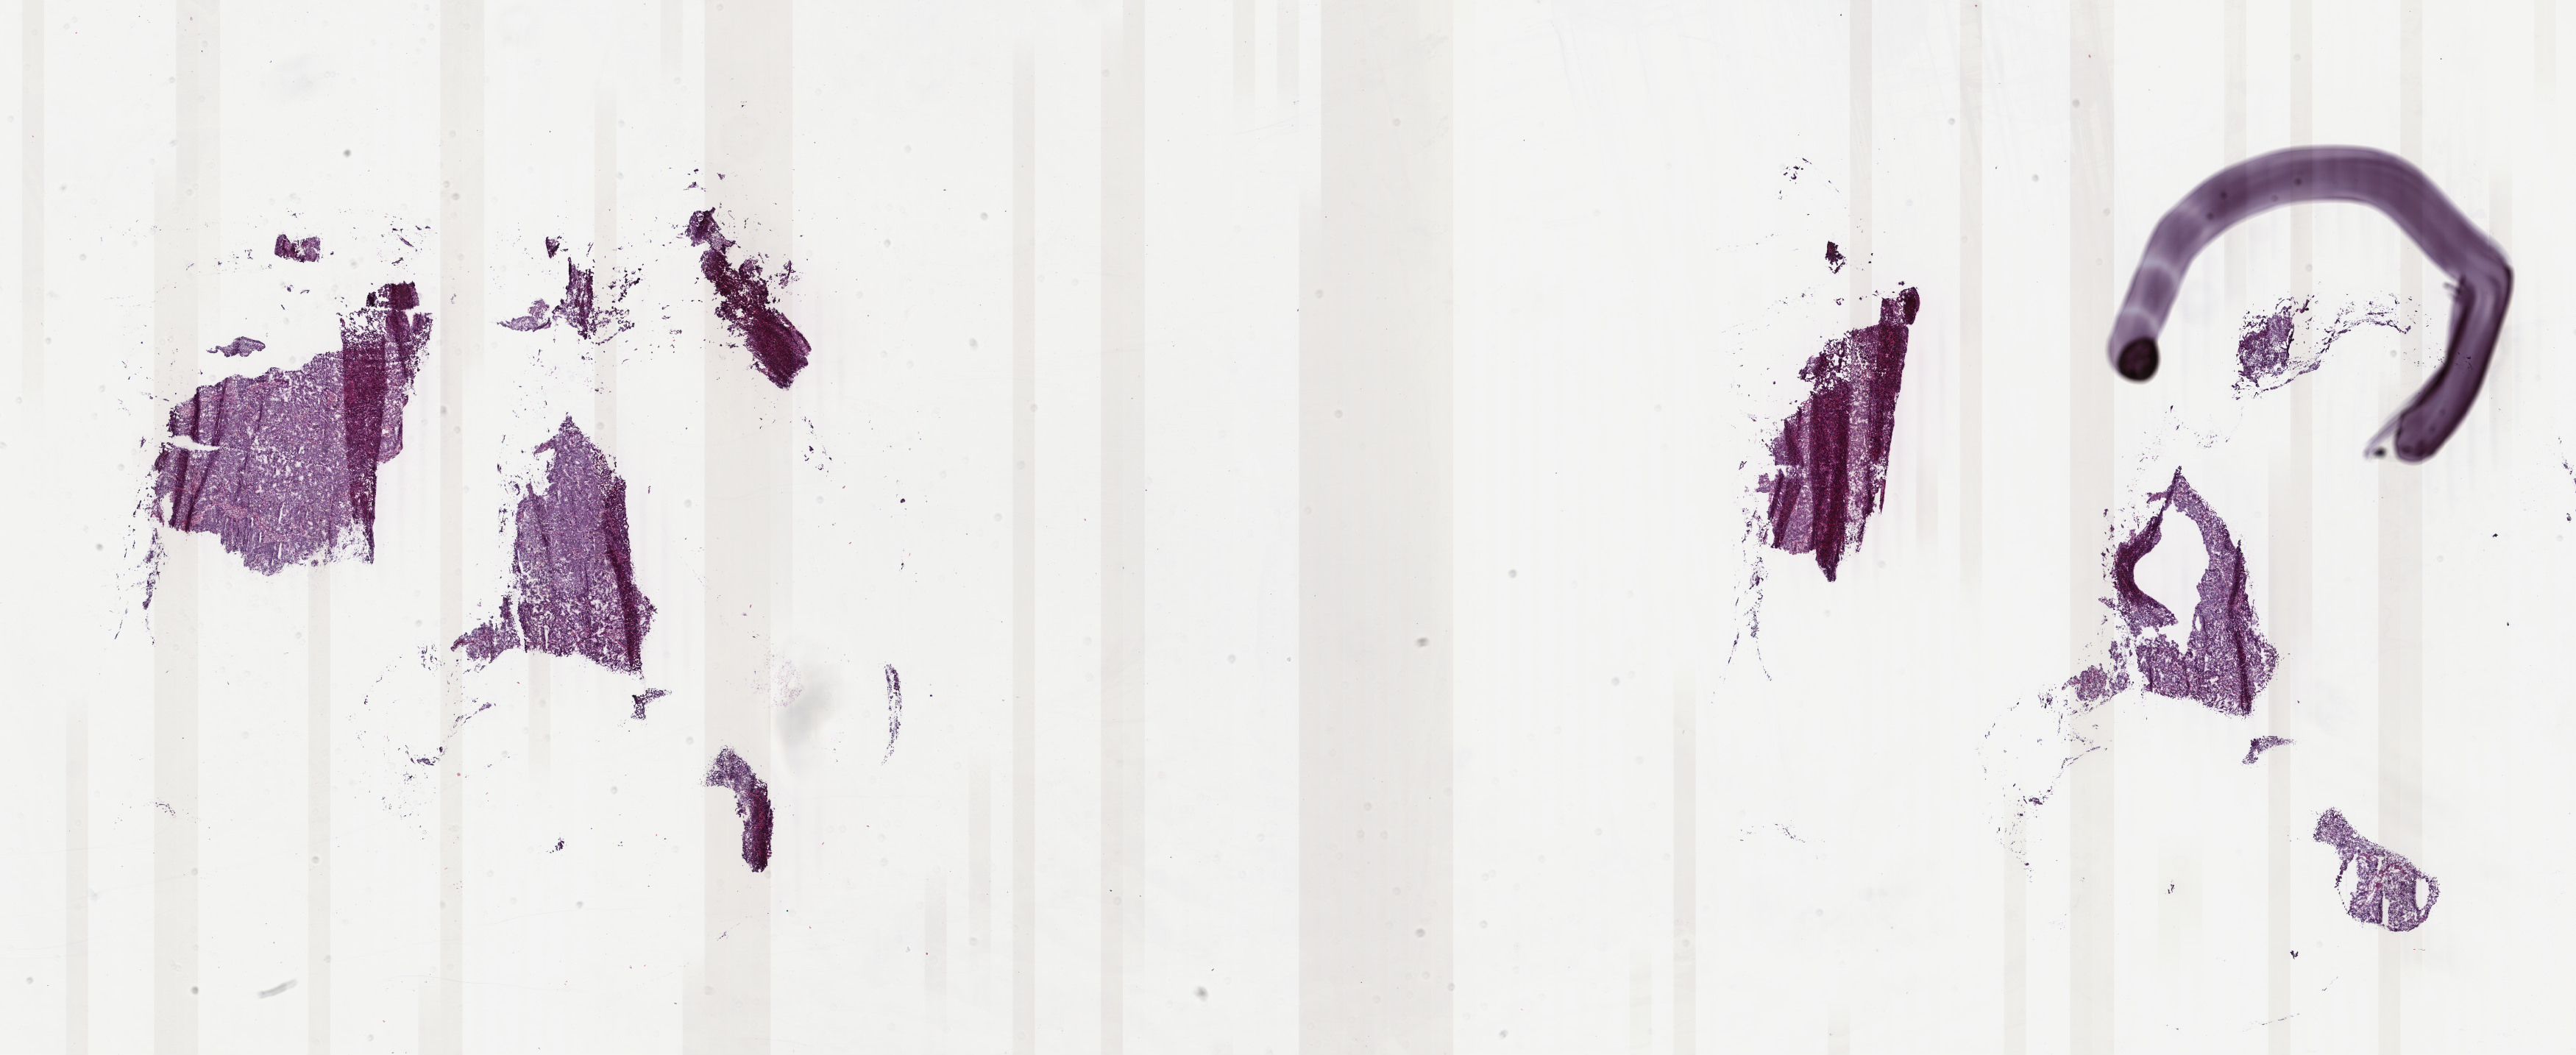
Digitized H&E tissue section (whole slide) — a low-resolution overview of the entire scanned area, about 27.8 x 11.4 mm (from a 40x scan). Frozen section from the bottom of the tissue portion. Uterus, primary tumour sample. Patient: female, age at initial diagnosis 52 years. Histologic grade: G2 (moderately differentiated). Pathologist review of this section (percent, as recorded): tumour cells 83%, tumour nuclei 90%, normal cells 0%, stromal cells 15%, necrosis 2%. Infiltration values recorded for this section: lymphocyte infiltration 4%, monocyte infiltration 0%, neutrophil infiltration 0%.
* pathologic diagnosis: Endometrioid adenocarcinoma, NOS (endometrium)
* FIGO stage: IC